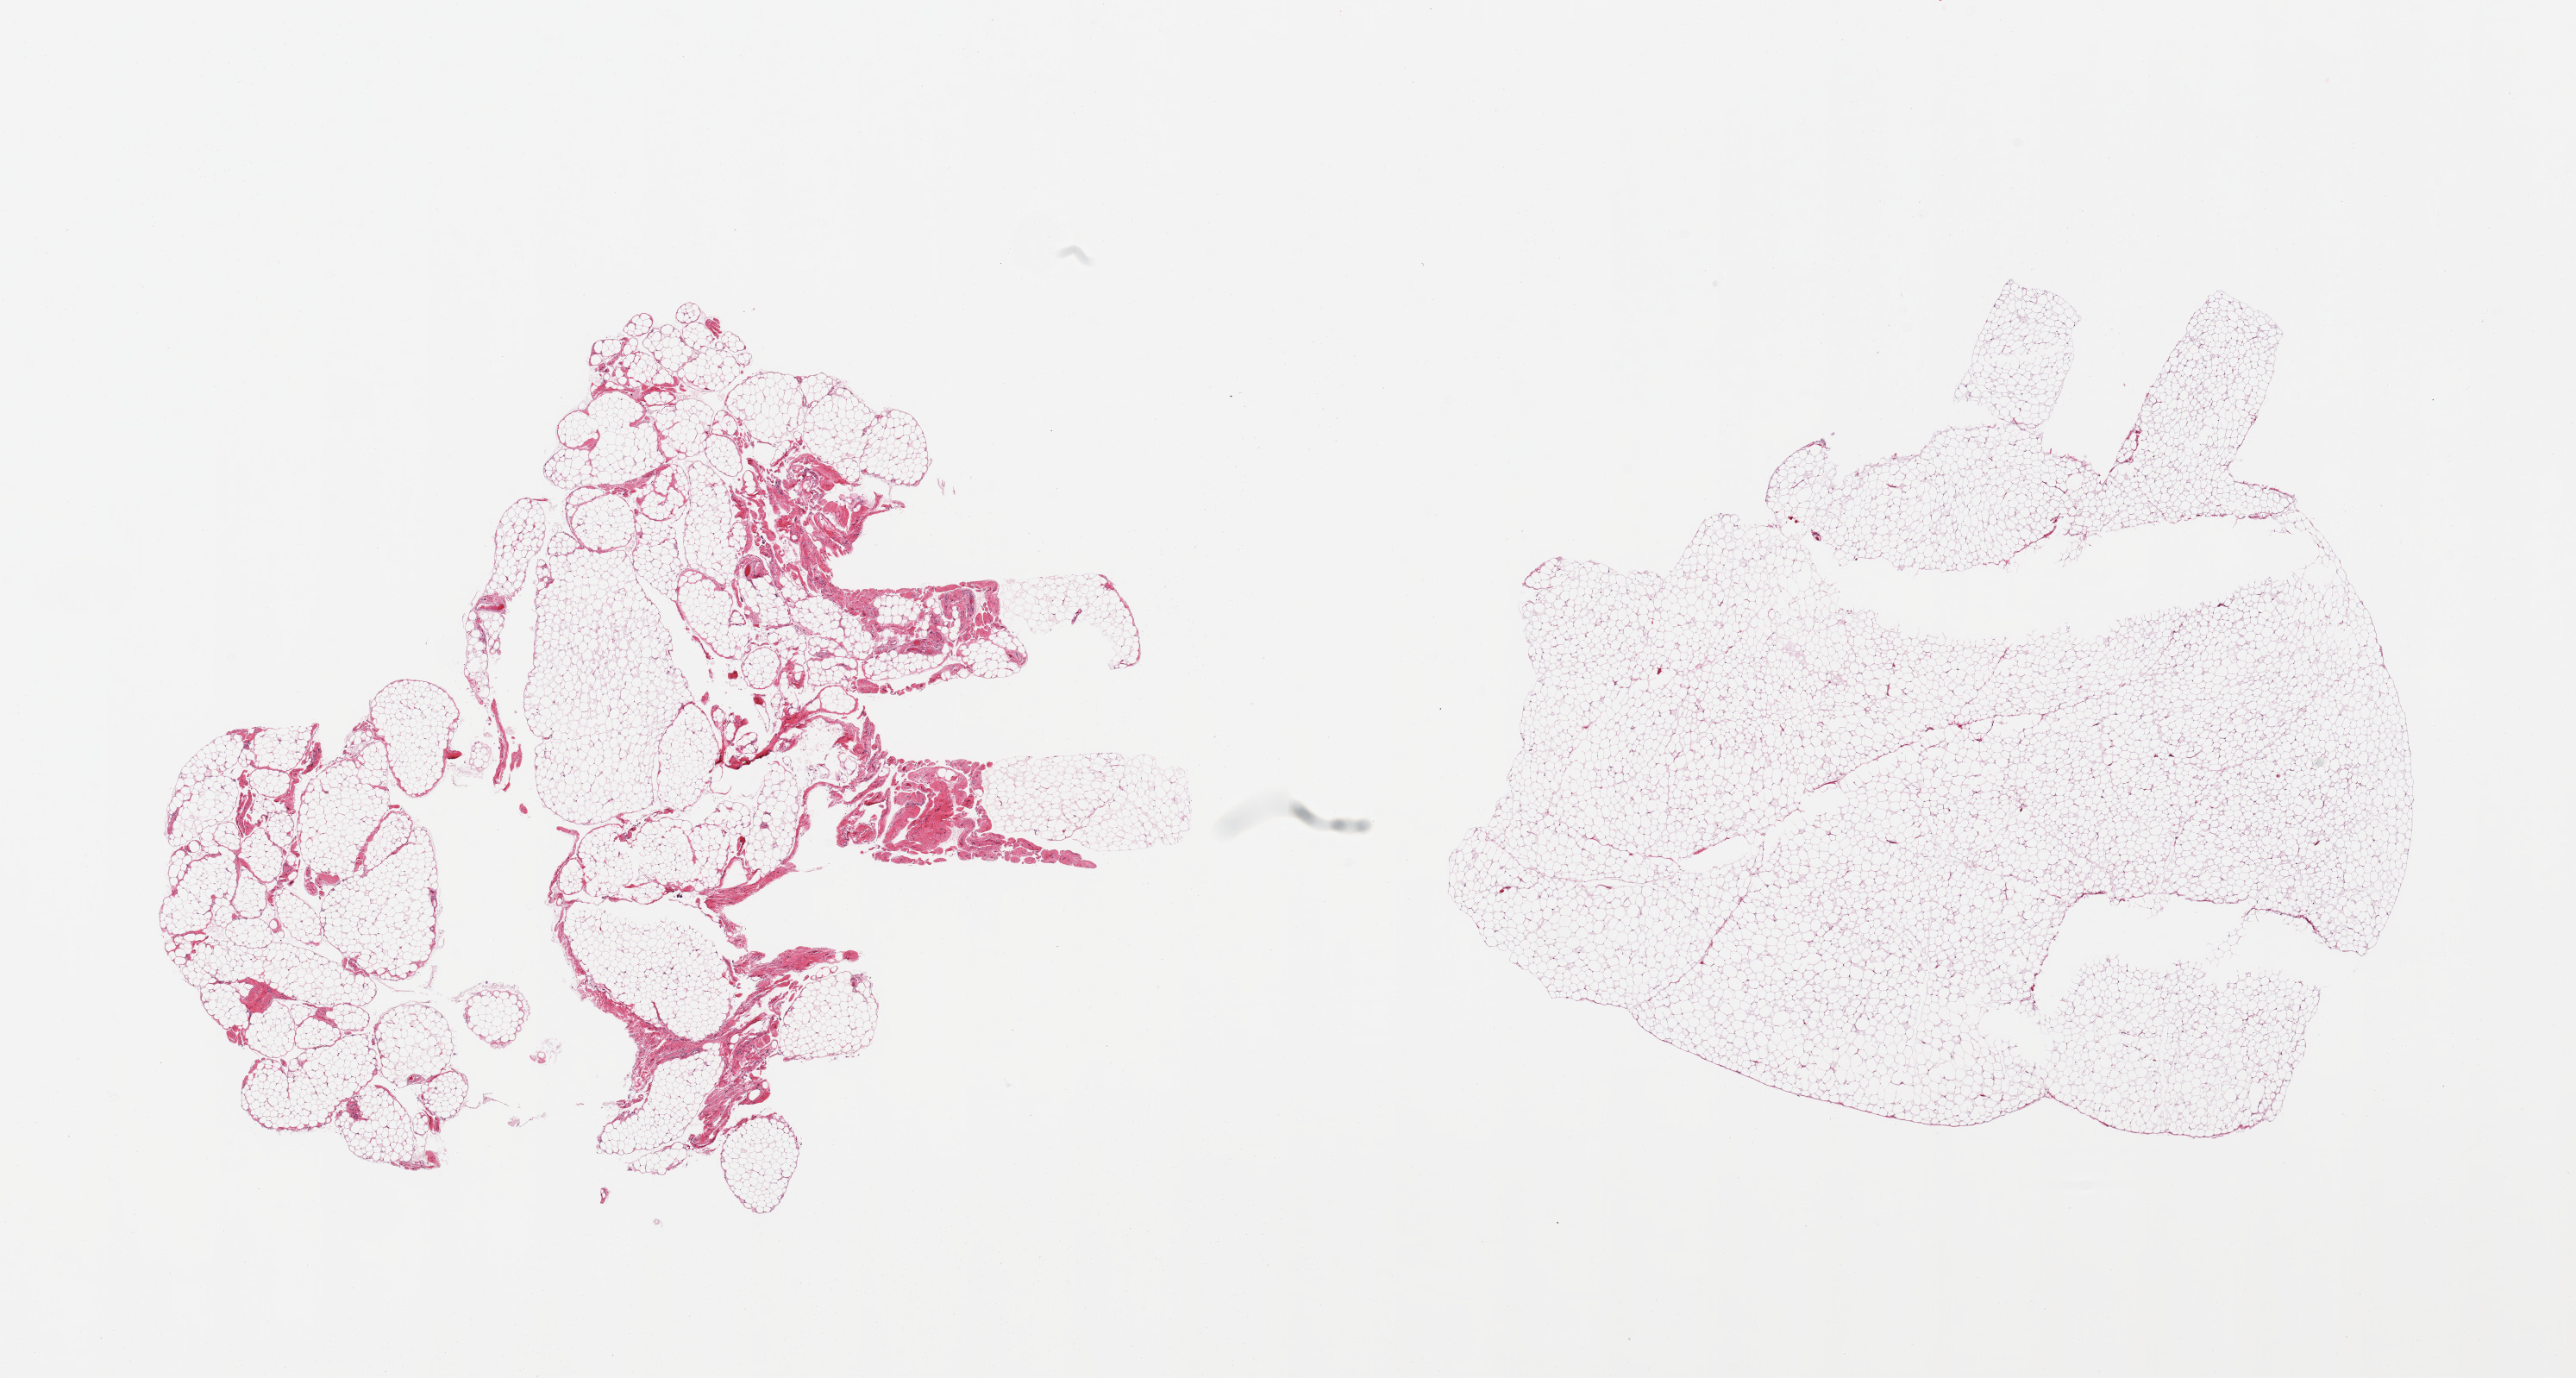
Whole-slide image, haematoxylin and eosin stain, shown as a low-resolution overview of the whole scanned area (about 23.6 x 12.6 mm); PAXgene-fixed paraffin-embedded (PFPE) section; section of omentum (target tissue); donor tissue sample. Donor sex: female.
Reviewer comment on this tissue sample: 2 pieces: 1 with 10% fibrous content.